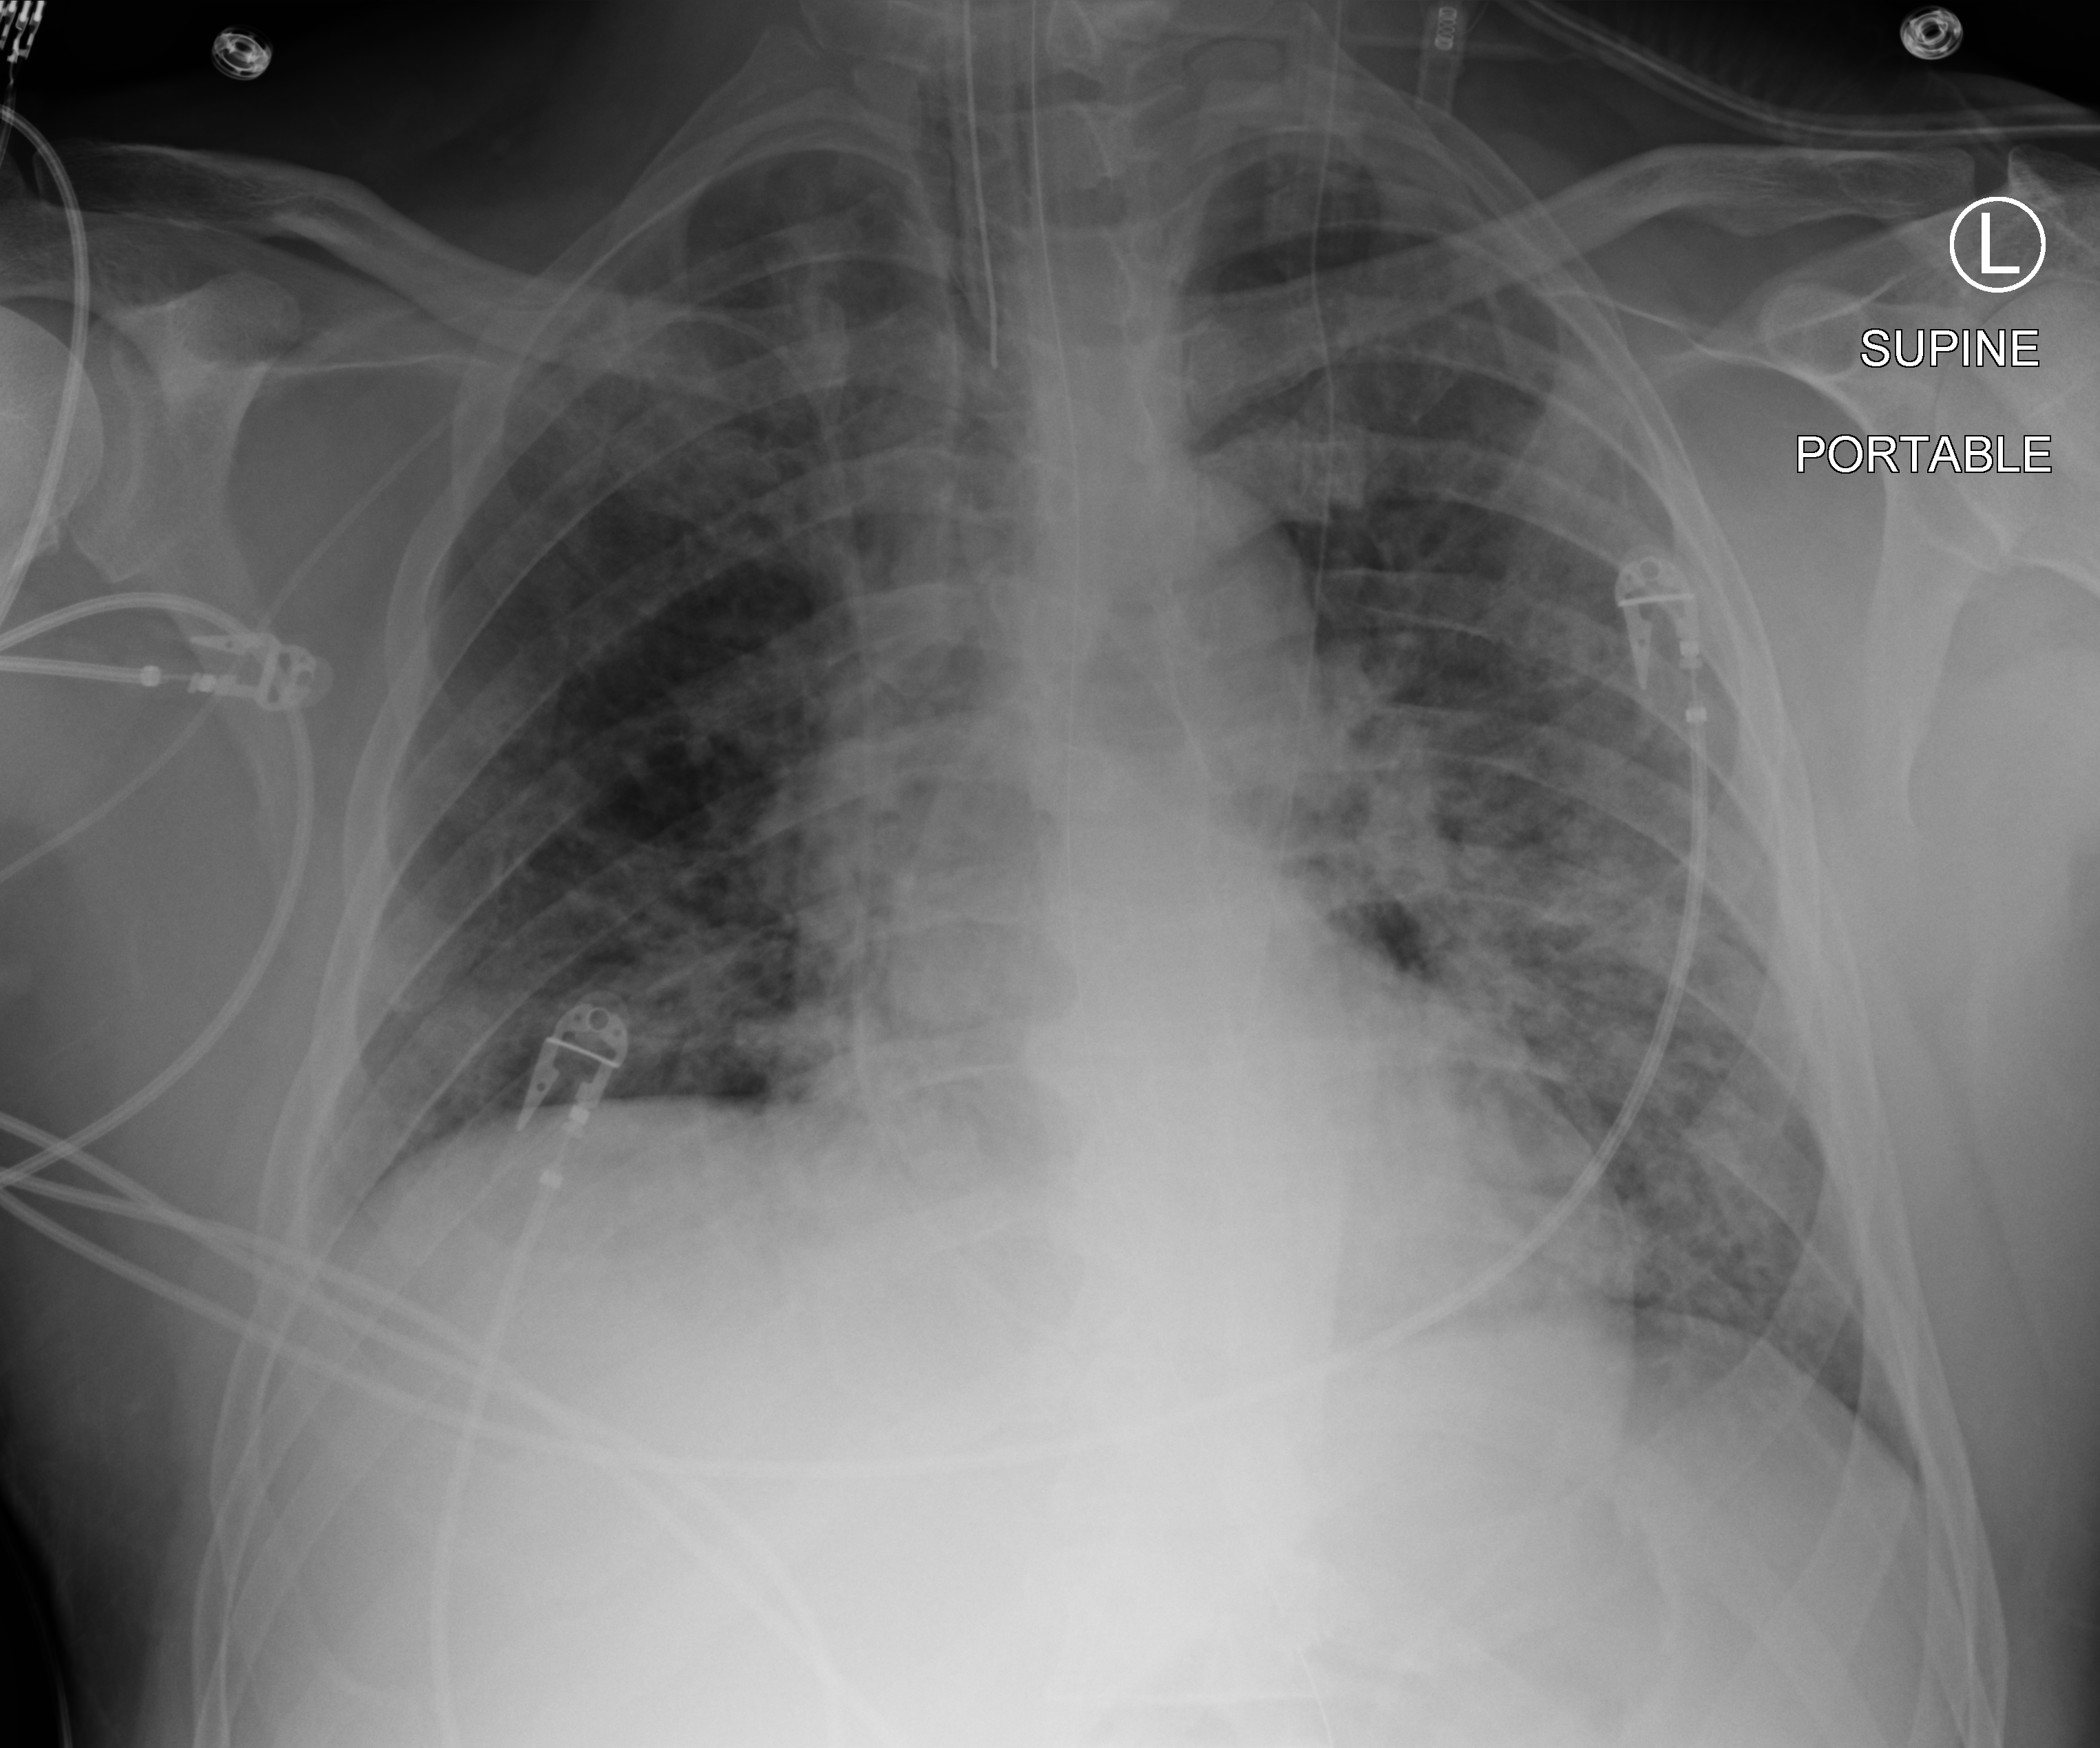
Portable chest radiograph, anteroposterior (AP) projection. Male patient hospitalised with COVID-19, age 18–59 years.
Hospital-stay facts (about this admission, not read from this image; timing relative to this image not recorded):
- mechanically ventilated during this hospital stay: yes